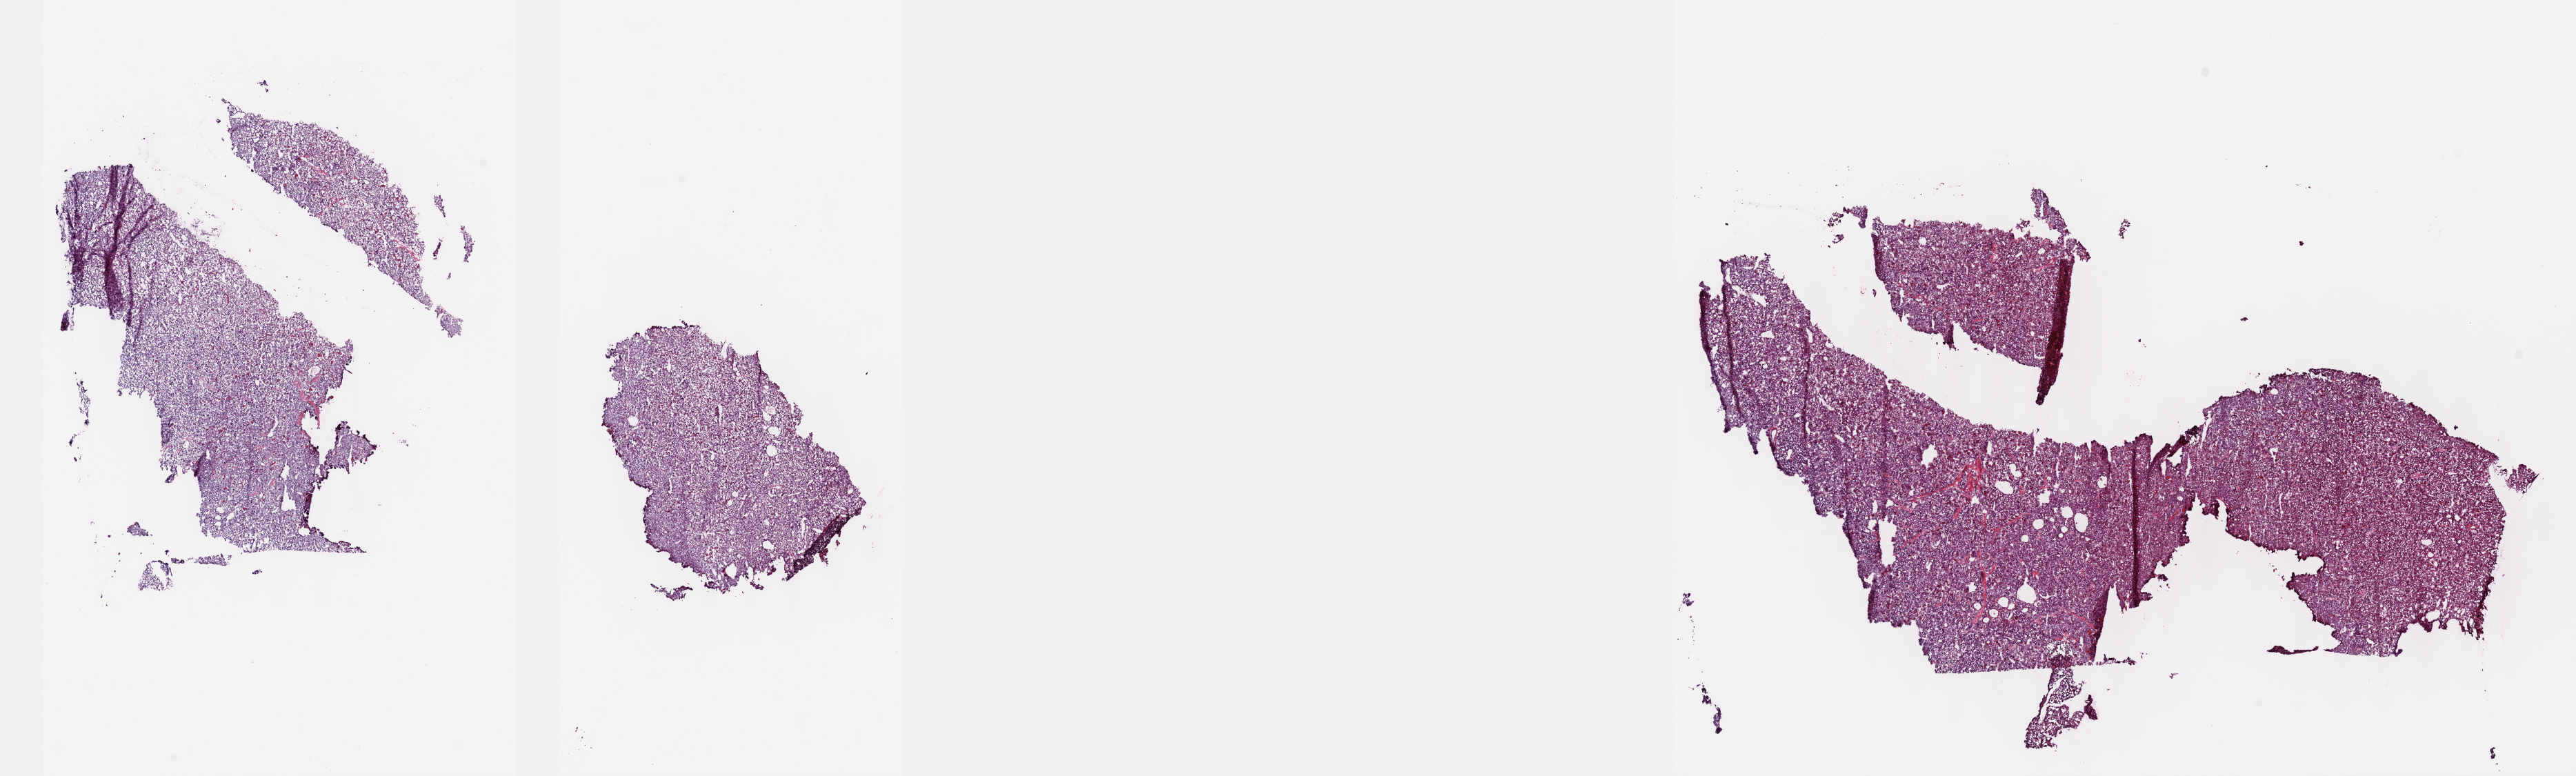
H&E-stained whole-slide image, a low-resolution overview of the entire scanned area, about 30.2 x 9.1 mm. Frozen section from the top of the tissue portion. Liver, primary tumour sample. Male patient; age at initial diagnosis 65 years. Pathologist review of this section (percent, as recorded): tumour cells 70%, tumour nuclei 70%.
Histologic diagnosis: Hepatocellular carcinoma, NOS.